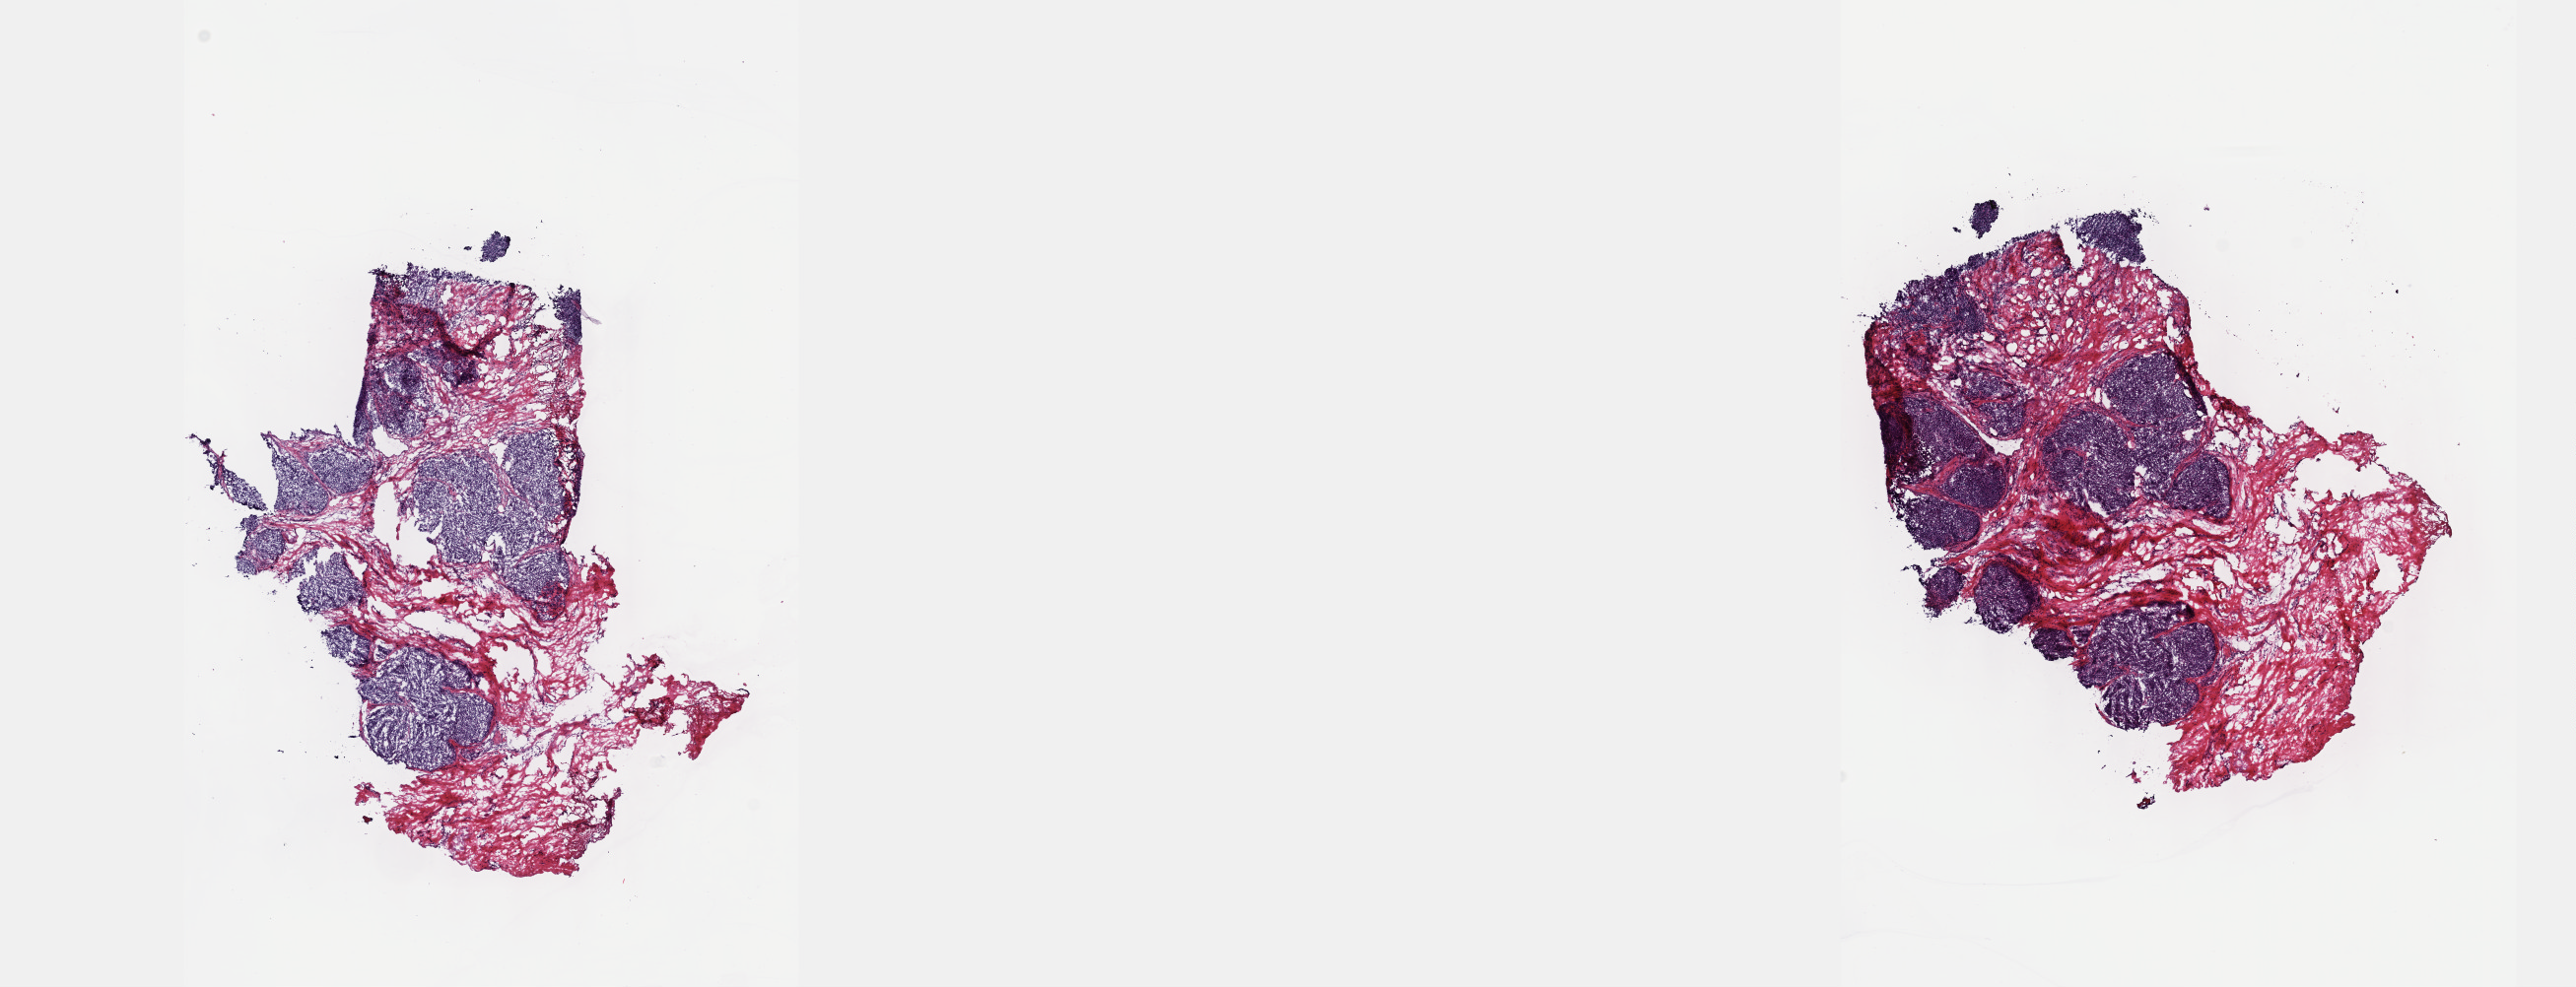
Whole-slide histology image, H&E, low-resolution overview of the scanned area, about 21.1 x 8.1 mm (slide scanned at 40x), frozen section from the top of the tissue portion, primary tumour sample from the thymus. Male, age 43 years at initial diagnosis. Composition of this section per pathologist review: tumour cells 100%, tumour nuclei 65%, normal cells 0%, stromal cells 0%, necrosis 0%. Infiltration values recorded for this section: lymphocyte infiltration 3%, monocyte infiltration 0%, neutrophil infiltration 0%.
Diagnosis: Thymoma, type B3, malignant.